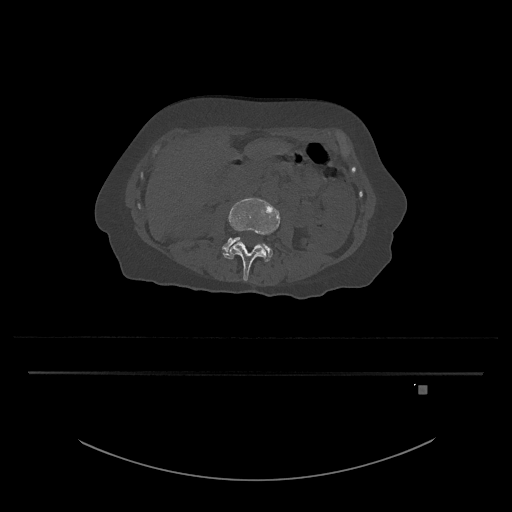
CT including the spine, one axial slice. Reconstruction kernel Br40s/3. Bone window (W 1800 / L 400 HU). 0.5 mm slice thickness. 512 × 512 image matrix. Patient: female, 57 years. From the clinical record (not read from this slice): primary cancer: cervical.
Outlined on this slice (semi-automatically segmented with operator editing):
- L3 vertebra: box from (x=223, y=198) to (x=280, y=281) px
- L4 vertebra: (x=222, y=237)–(x=273, y=262)